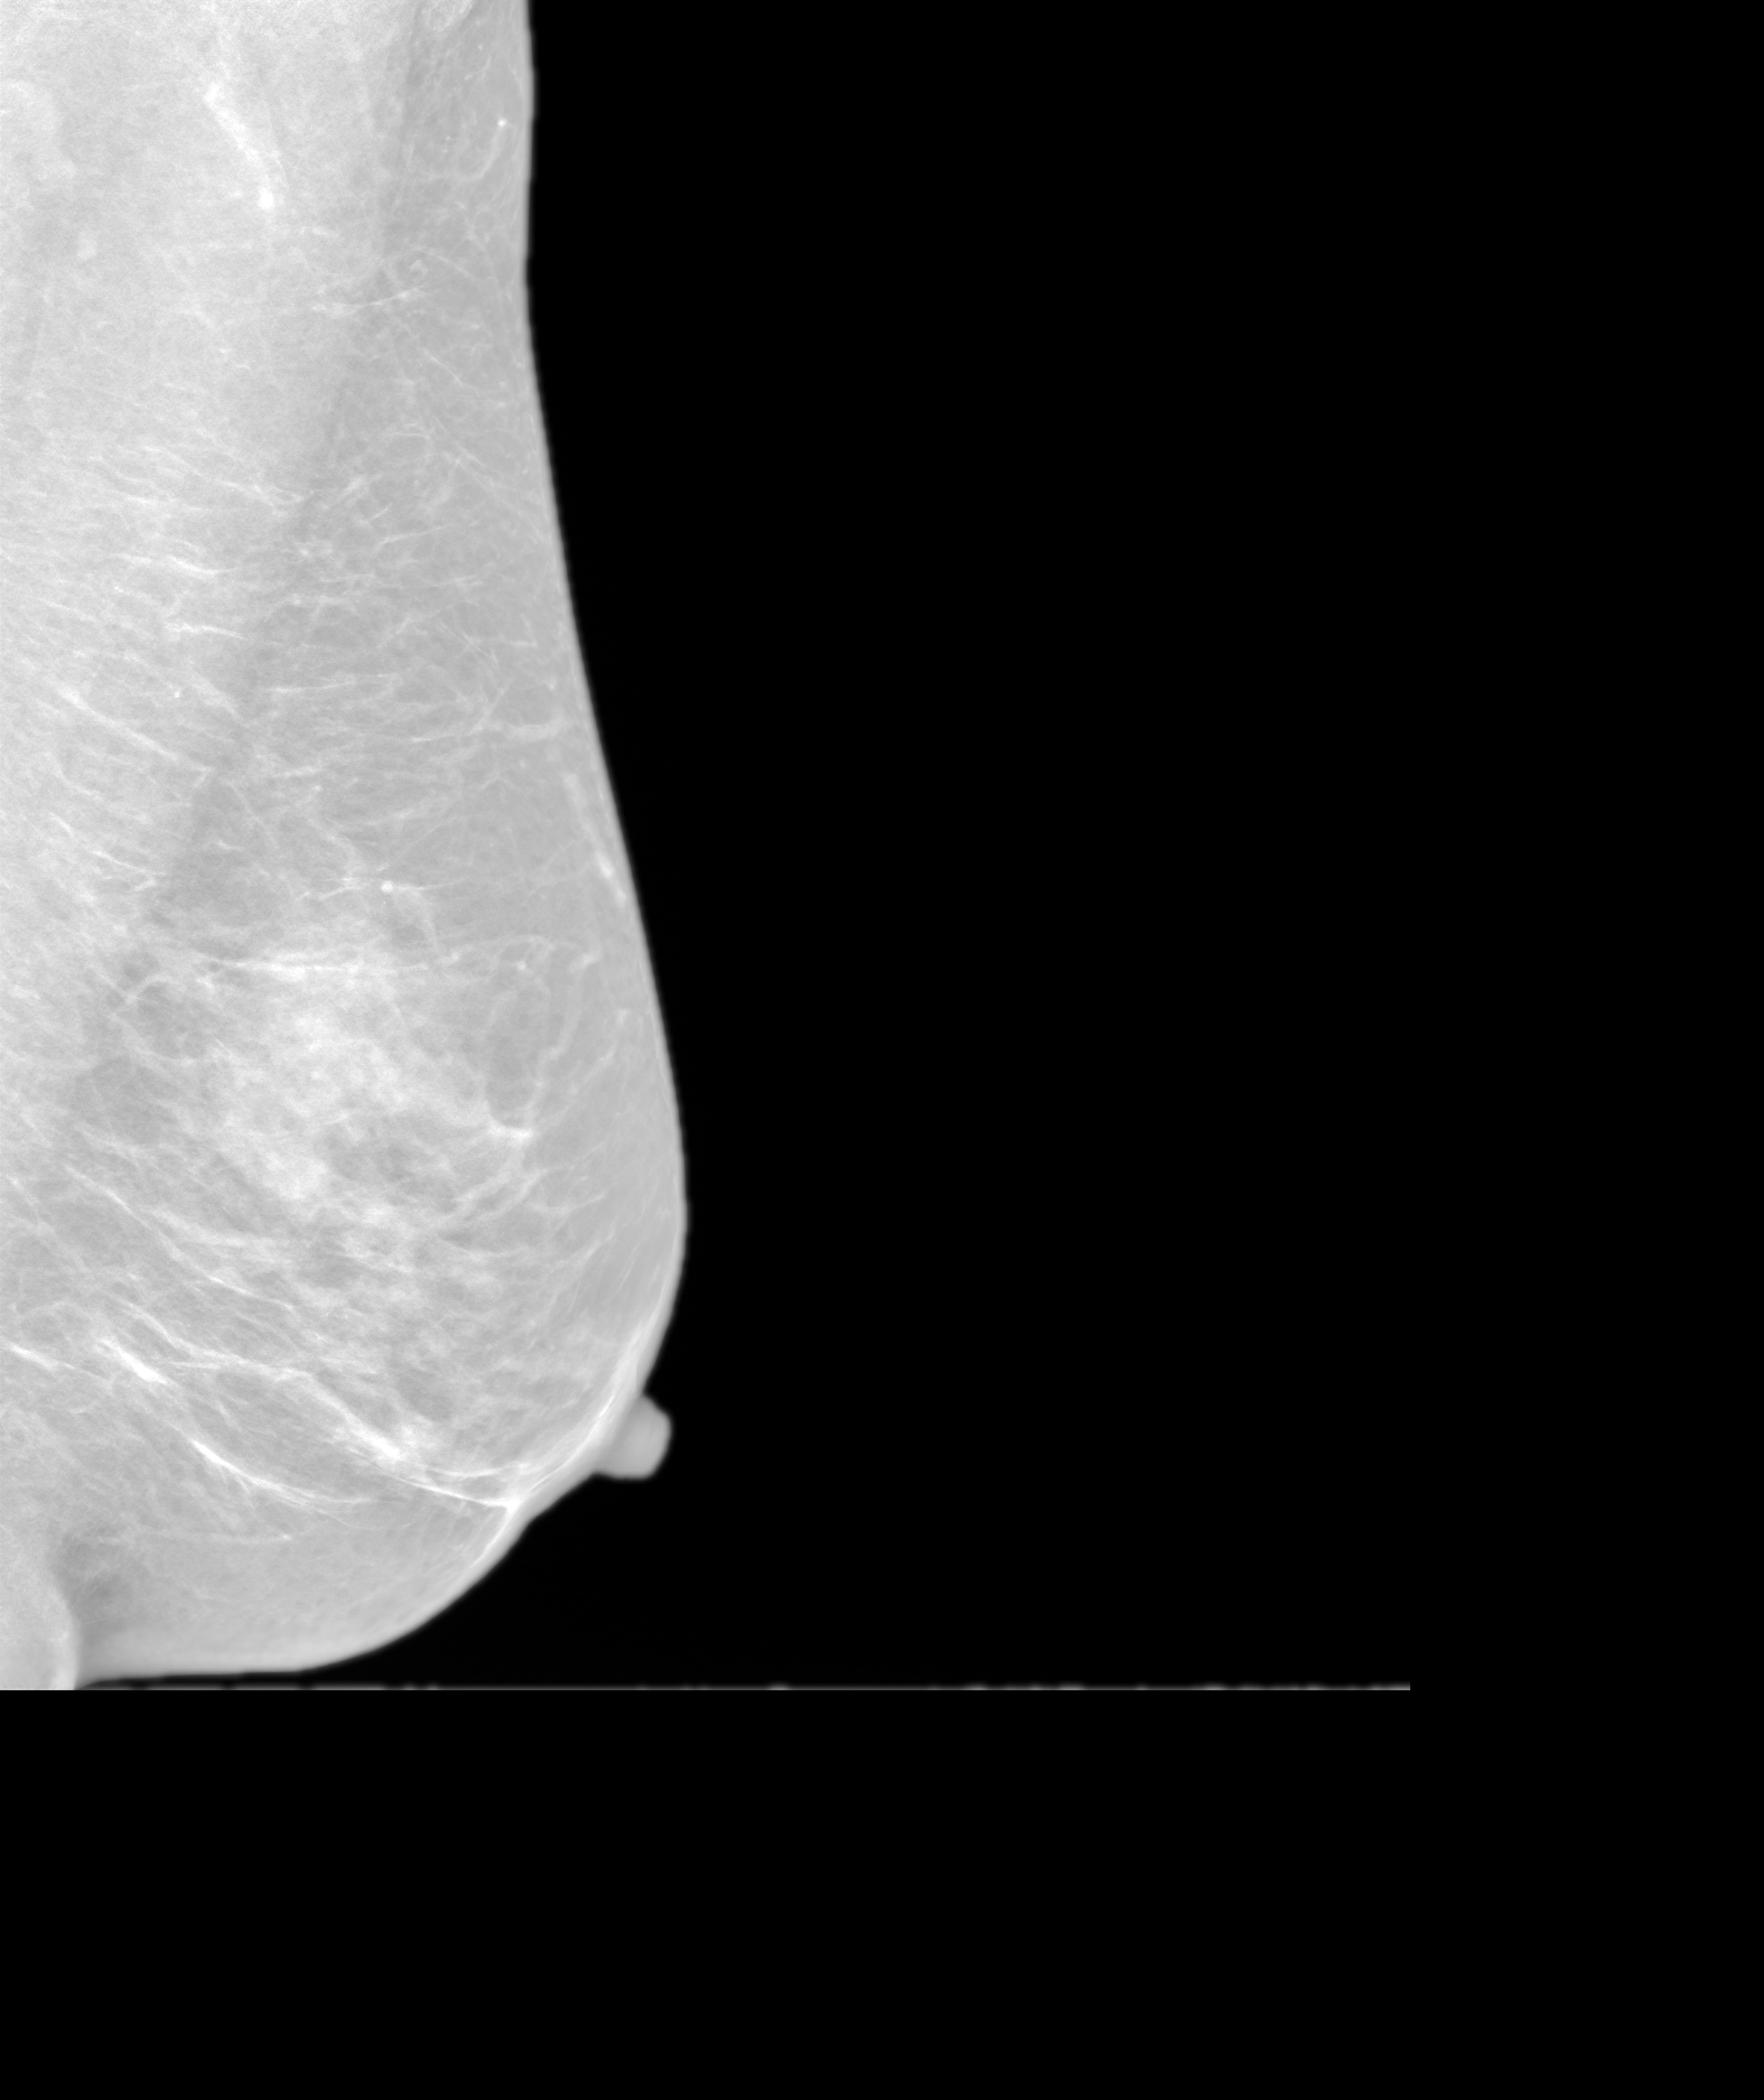
Annual screening mammography examination. Patient aged 49 years (female).
Image type: synthesized 2-D view from tomosynthesis. Breast: left. Projection: MLO view.